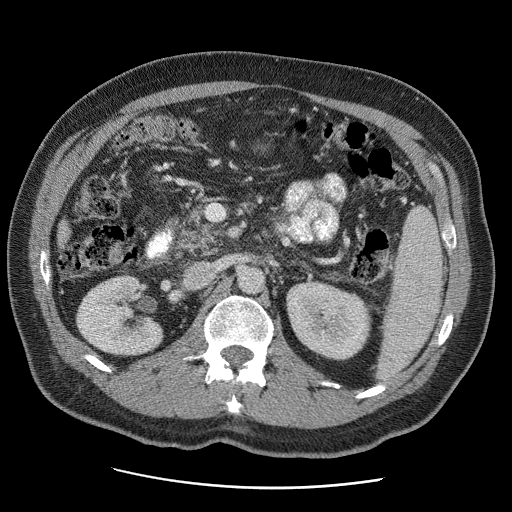
Contrast-enhanced abdominal CT (liver protocol), one axial slice; position 6 of 81 along the scan axis; reconstruction kernel STANDARD; soft-tissue window (W 400 / L 40 HU); 512 × 512 image matrix, field of view 380 × 380 mm. Case-level facts recorded for this patient, not image findings: diagnosis: hepatocellular carcinoma (patient treated with transarterial chemoembolisation; whether this scan precedes or follows treatment is not stated here); TNM stage (as recorded): Stage-IIIA; Child-Pugh class: A; tumour differentiation: moderately differentiated; tumour size: 5.5 cm.
Annotated regions visible in this slice (semi-automatic segmentation, software-assisted and operator-edited):
- liver parenchyma outside the tumour (the mass and vessels are separate outlines, so this box may not span the whole liver): bounding box (x1, y1, x2, y2) in pixels: (56, 218, 69, 247)